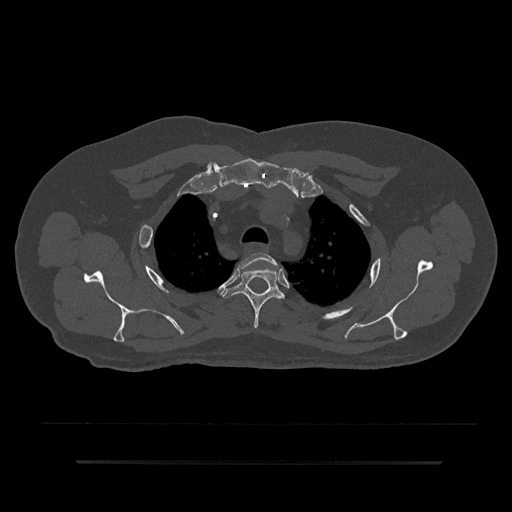
CT including the spine, one axial slice. Position 663 of 797 along the scan axis. Reconstruction kernel Br40s/3. 120 kVp. Bone window (W 1800 / L 400 HU). 512 × 512 image matrix. Male patient, age 59 years. From the clinical record (not read from this slice): primary cancer: bile ducts.
Structures marked on this image (semi-automatic segmentation, software-assisted and operator-edited):
- T2 vertebra: bounding box [x1, y1, x2, y2] px = [236, 252, 278, 269]
- T3 vertebra: [223, 268, 285, 328]